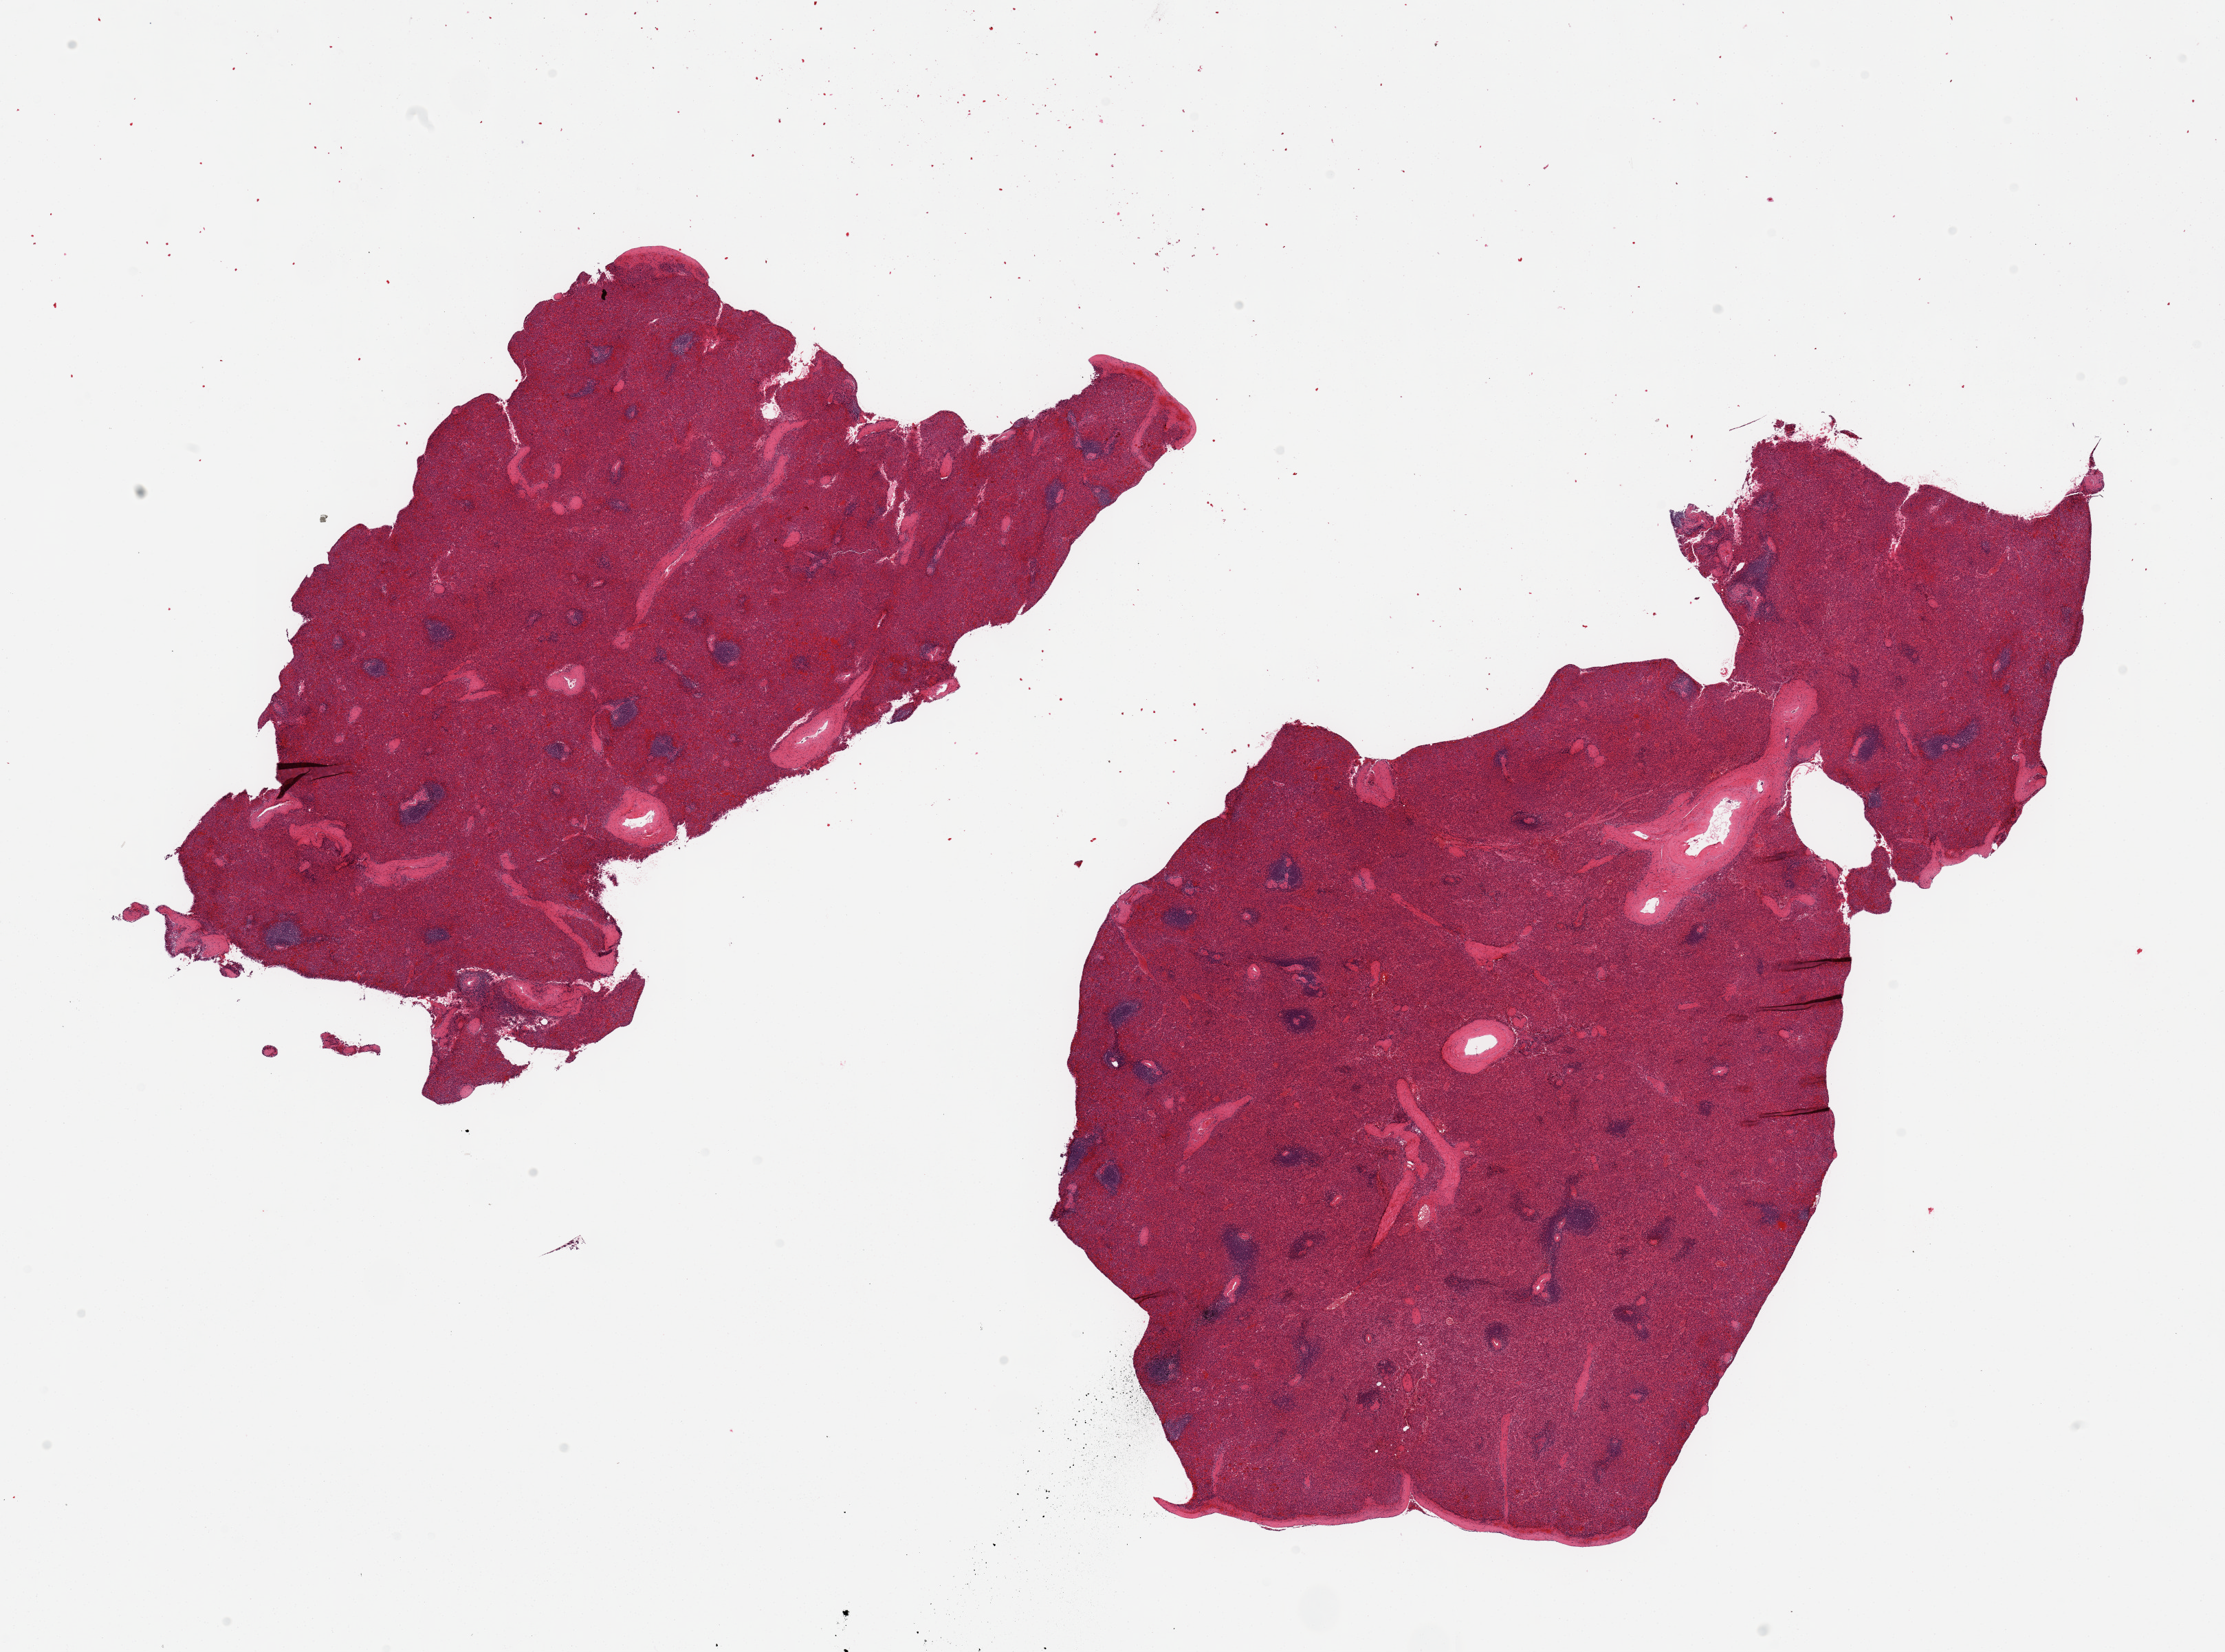
Whole-slide image, haematoxylin and eosin stain — low-resolution overview of the scanned area, about 25.6 x 19.0 mm (acquisition: 20x scan); PAXgene-fixed paraffin-embedded (PFPE) section; sampled site (target tissue): spleen; donor tissue sample. Donor: male.
Review note (as recorded): 2 pieces, no abnormalities.